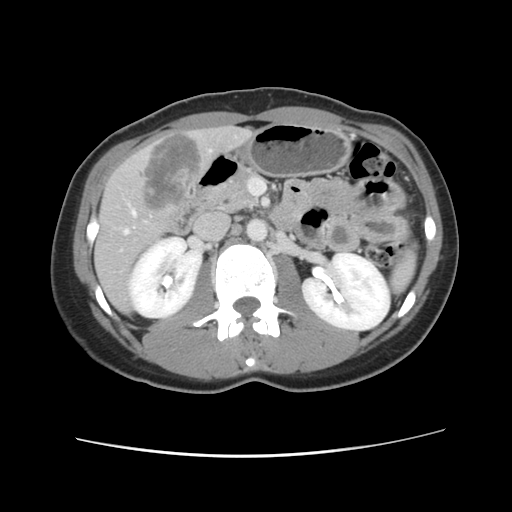
Contrast-enhanced abdominal CT, one axial slice; position 43 of 134 along the scan axis; intravenous contrast given; soft-tissue window (W 400 / L 40 HU); 2.5 mm slice thickness; 512 × 512 image matrix, field of view 339 × 339 mm. Female patient, age 33 years. From the clinical record (not read from this slice): diagnosis: colorectal cancer liver metastases, imaged before liver resection; multiple liver metastases: yes; largest metastasis: 4.5 cm.
Annotated regions visible in this slice (outlined manually by an expert reader):
- hepatic veins: bounding box (x1, y1, x2, y2) in pixels: (124, 150, 212, 234)
- liver: (95, 127, 252, 311)
- planned liver remnant (the part of the liver to remain after resection): (94, 239, 133, 311)
- liver metastasis: (136, 133, 205, 211)